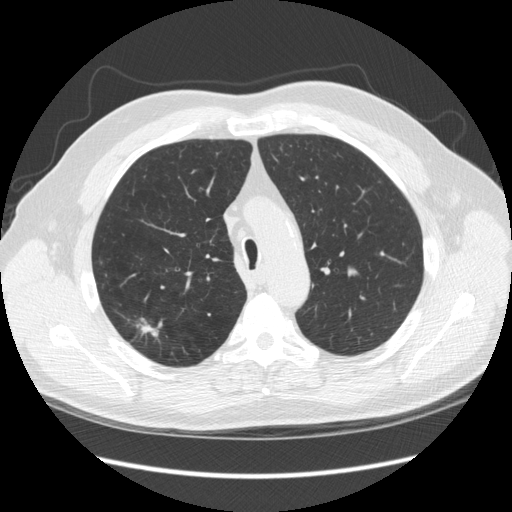
Low-dose screening chest CT, one axial slice; position 183 of 248 along the scan axis; reconstruction kernel STANDARD; 120 kVp; lung window (W 1500 / L -600 HU); 2.5 mm slice thickness; 512 × 512 image matrix, field of view 380 × 380 mm.
Outlined on this slice (manually delineated by an expert):
- lesion 1 (tumor, upper lobe of right lung): bounding box [x1, y1, x2, y2] px = [140, 325, 159, 337]